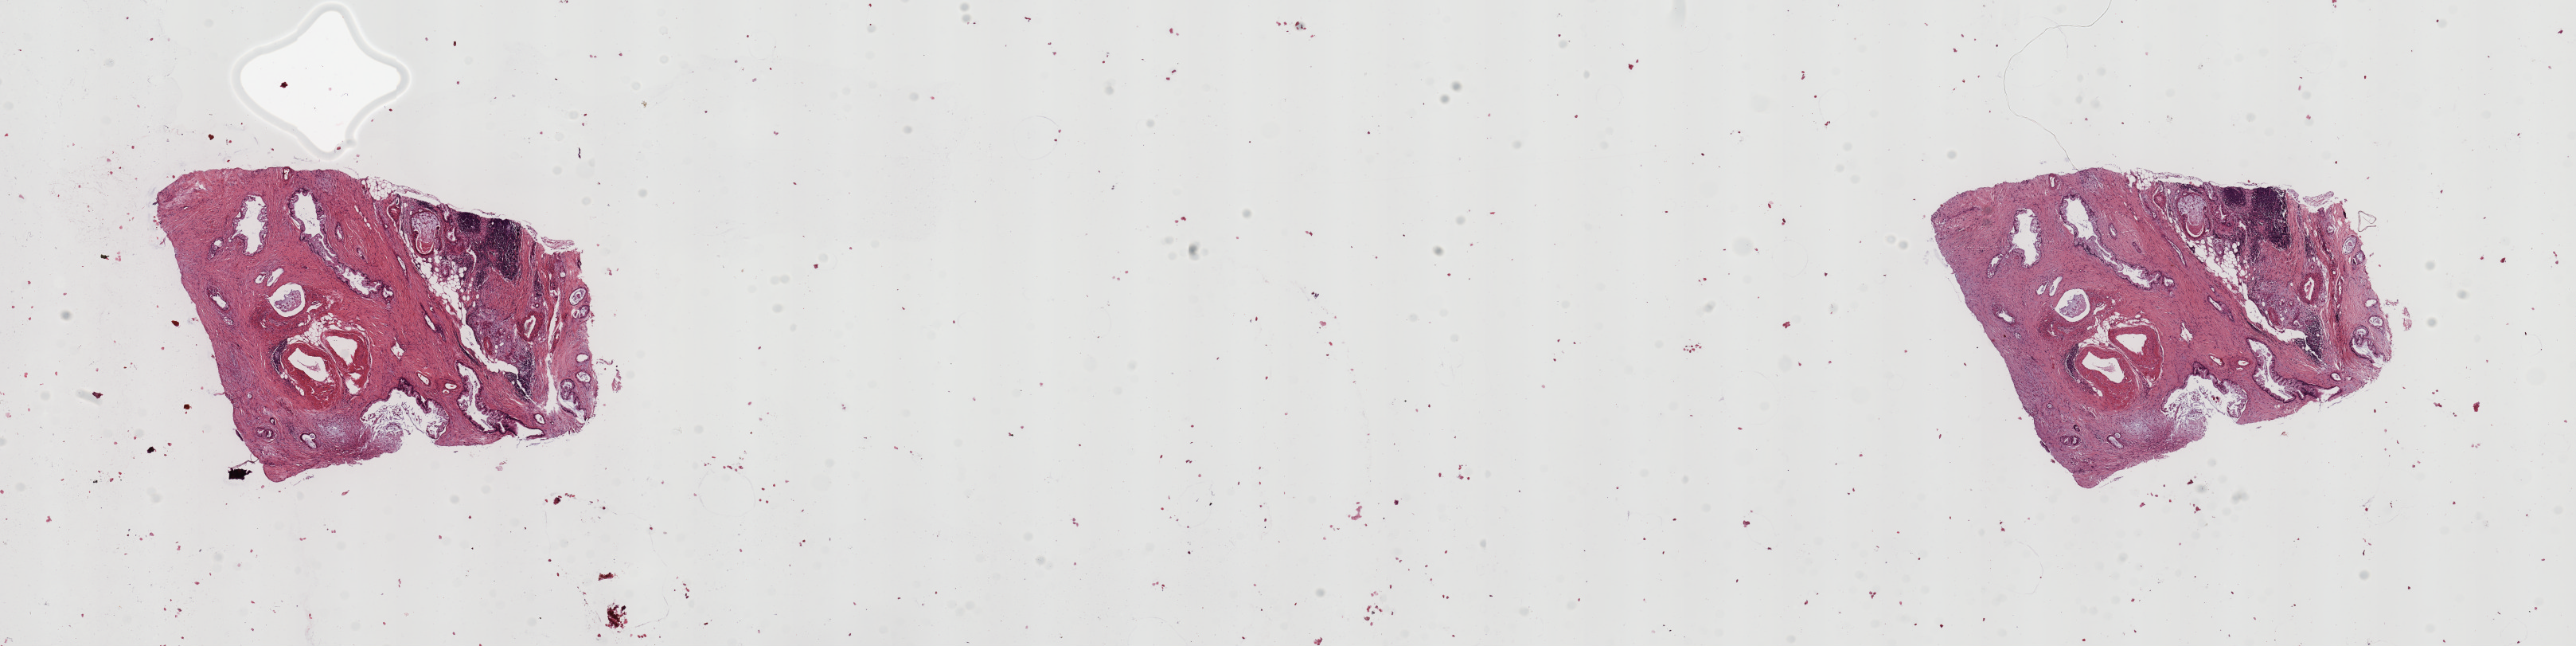
H&E whole-slide image — a low-resolution overview of the entire scanned area, about 25.6 x 6.4 mm (from a 20x scan); tumour tissue sample, sampled site: pancreas. 62-year-old female patient. Histologic grade: G2 (moderately differentiated). Slide review estimates, as recorded: tumour nuclei 20%, necrosis 2%.
Primary tumour site (as recorded): head. Diagnosis: Infiltrating duct carcinoma, NOS. AJCC pathologic stage: III.